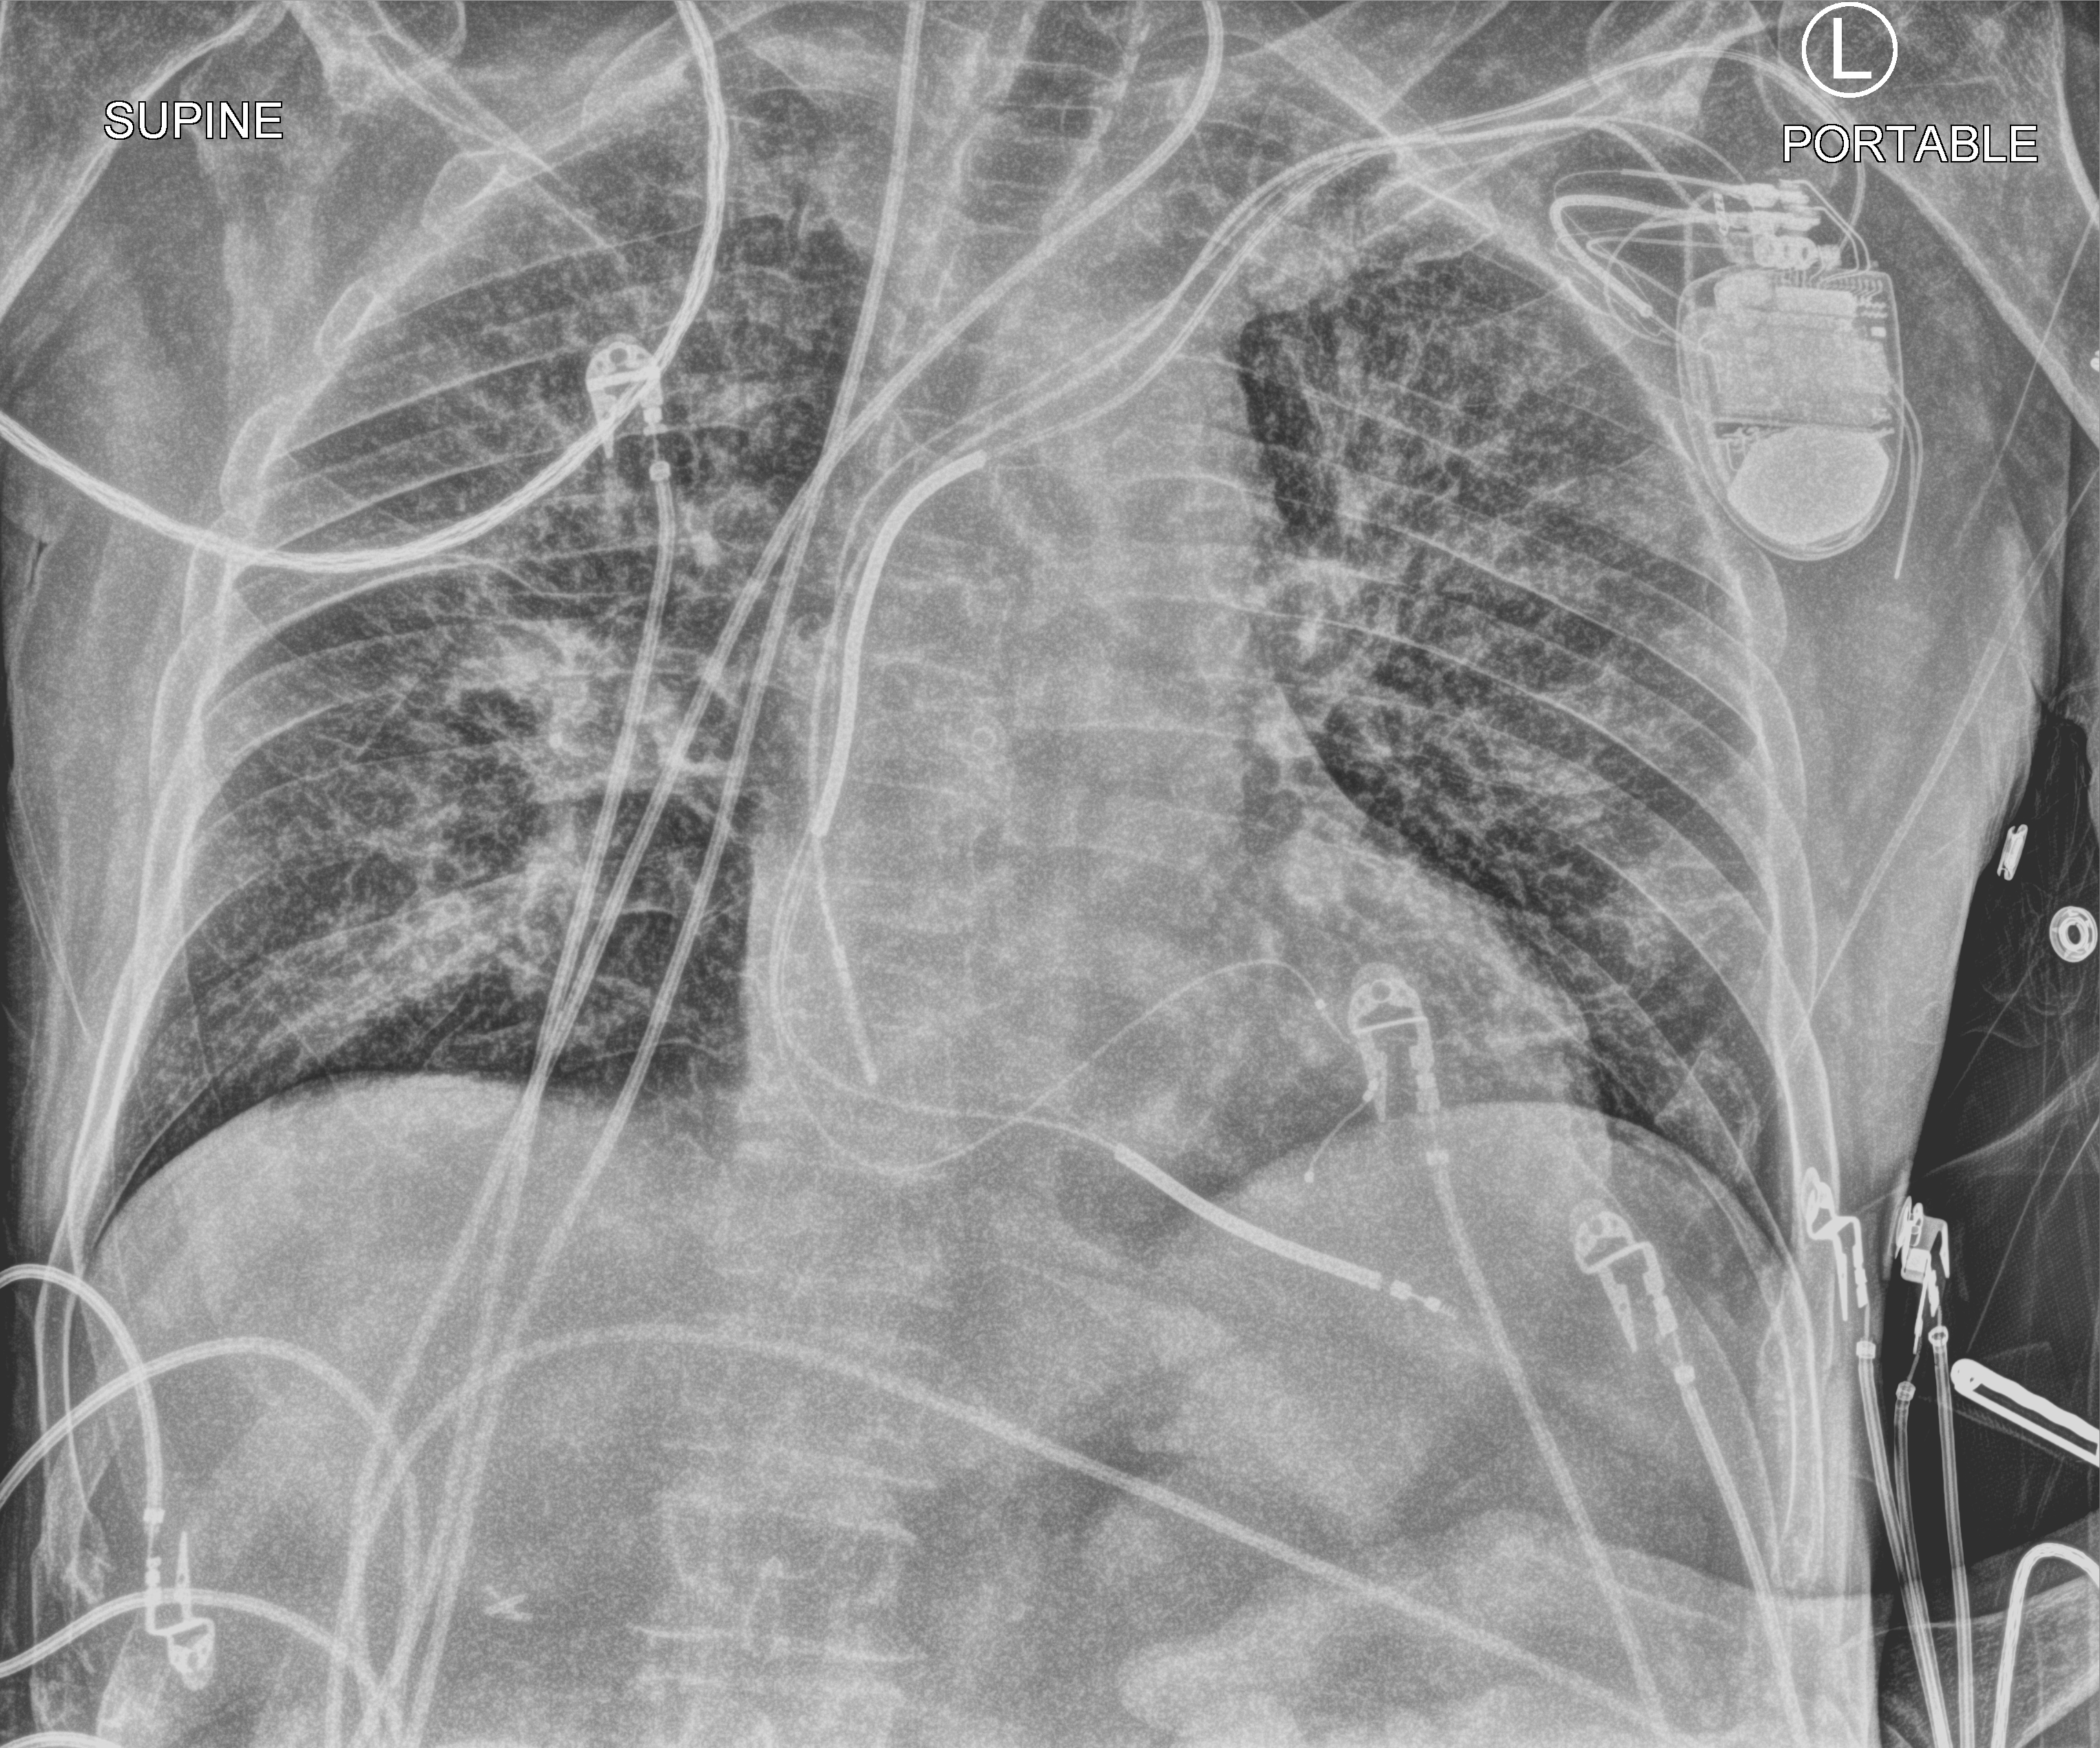
Chest X-ray (portable); anteroposterior (AP) projection. Male patient hospitalised with COVID-19, age 75–90 years.
Hospital-stay facts (about this admission, not read from this image; timing relative to this image not recorded): mechanically ventilated during this hospital stay: no; admitted to intensive care during this hospital stay: no.